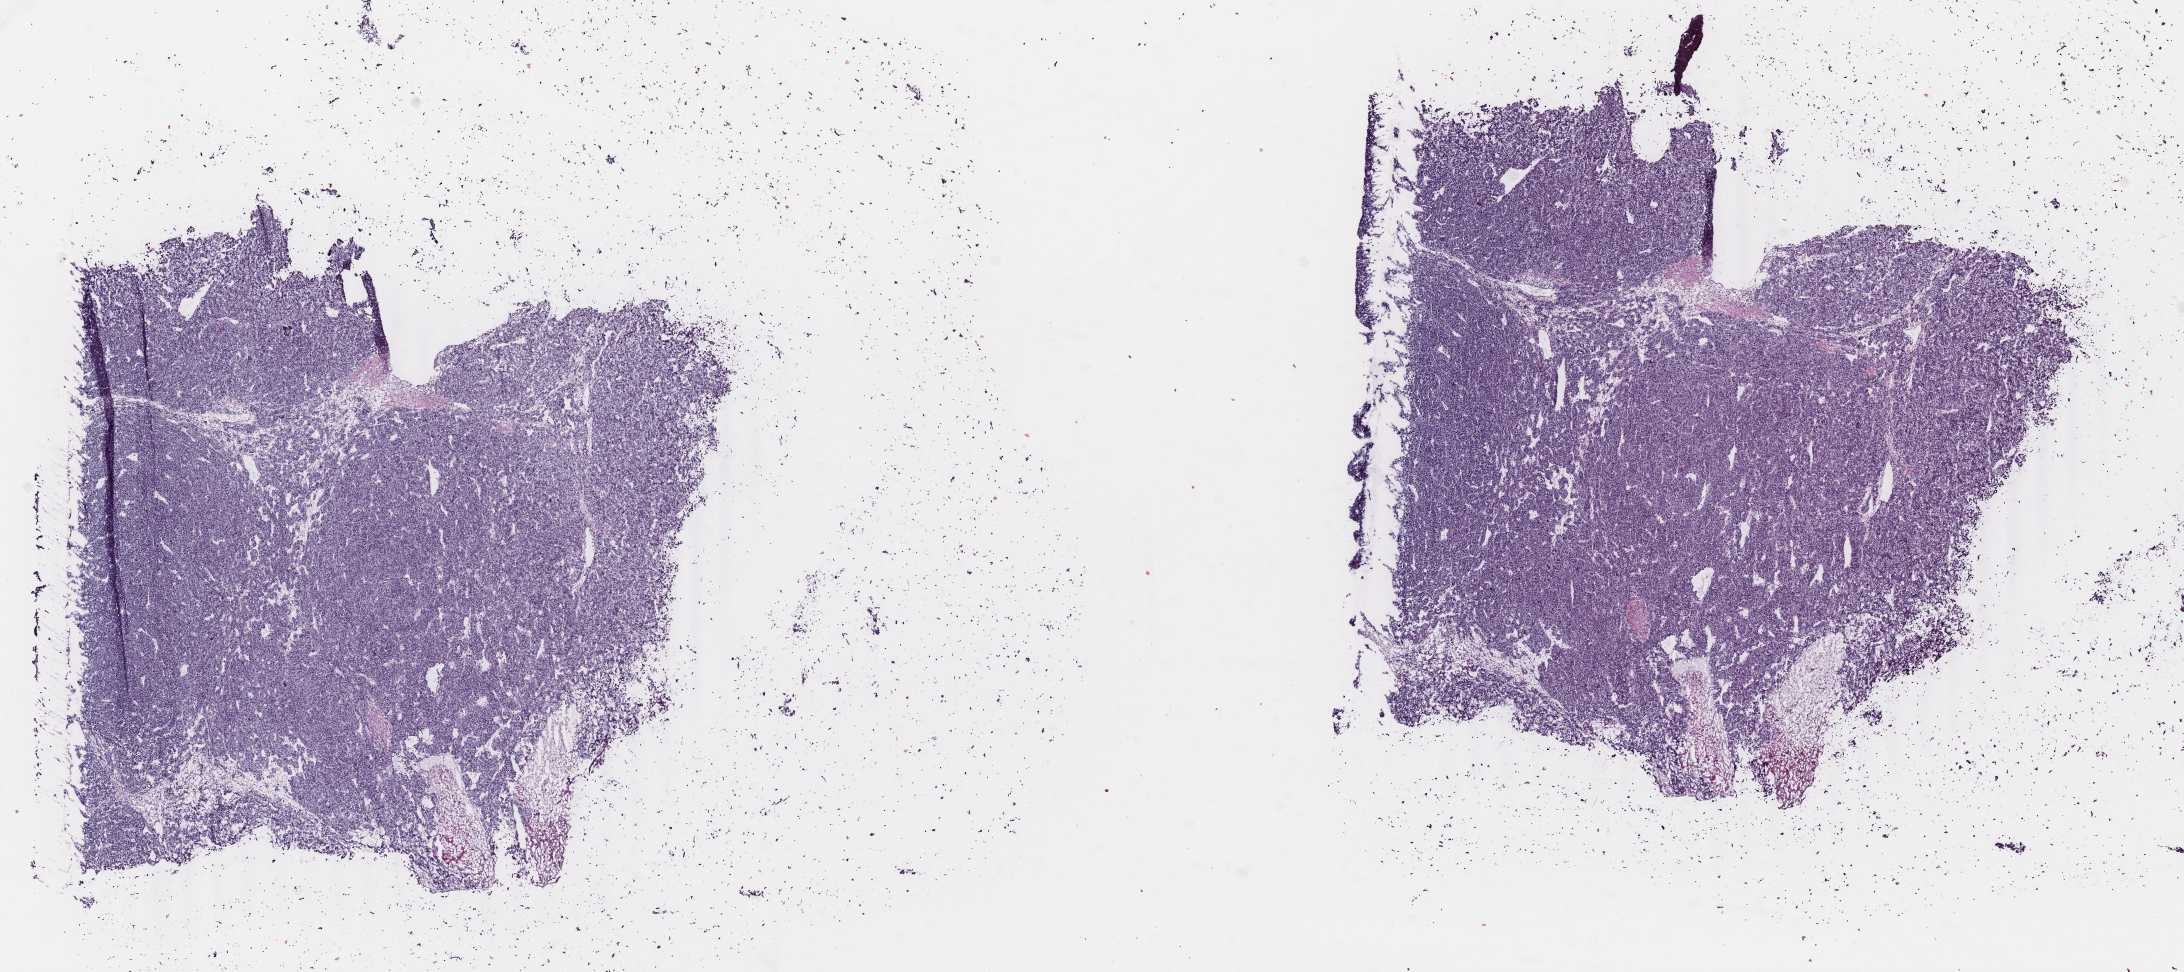
Whole-slide histology image, Hematoxylin and eosin (H&E) stained, shown as a low-resolution overview of the whole scanned area (about 17.4 x 7.7 mm, slide scanned at 40x). Frozen section. Primary tumour sample from the liver. Patient: male, age at initial diagnosis 76 years. Histologic grade: G3 (poorly differentiated). Composition of this section per pathologist review: tumour cells 90%, tumour nuclei 90%, normal cells 0%, stromal cells 10%, necrosis 0%. Inflammatory infiltration, as recorded: lymphocyte infiltration 2%, monocyte infiltration 0%, neutrophil infiltration 0%.
Histologic diagnosis: Hepatocellular carcinoma, NOS.